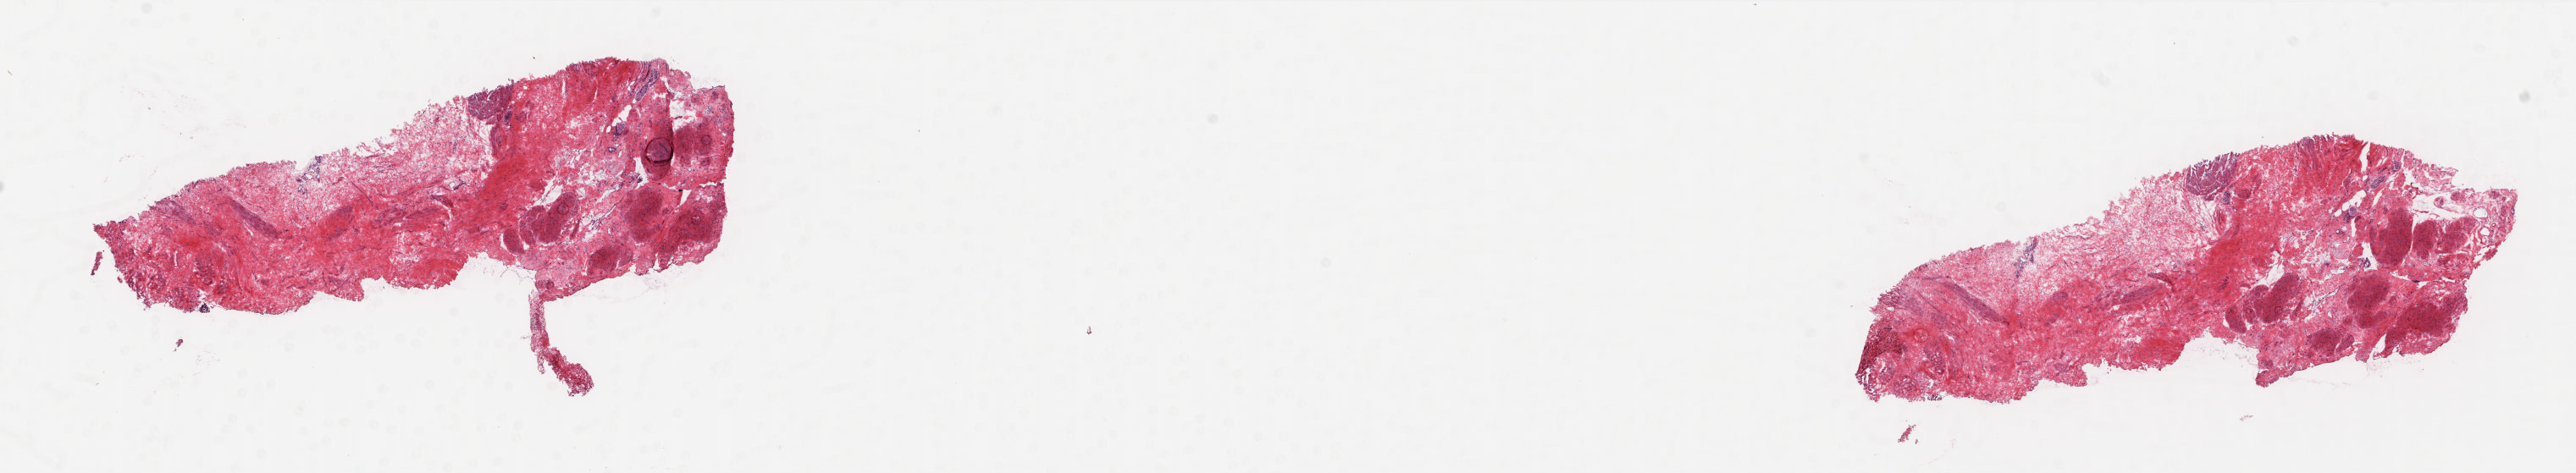
H&E-stained whole-slide image — a low-resolution overview of the entire scanned area, about 24.5 x 4.5 mm (acquisition: 20x scan); frozen section from the top of the tissue portion; bladder, solid tissue normal (non-tumour tissue) sample. Patient: female, age at initial diagnosis 75 years. Pathologist review of this section (percent, as recorded): tumour cells 0%, tumour nuclei 0%, normal cells 100%, stromal cells 0%, necrosis 0%. Infiltration values recorded for this section: lymphocyte infiltration 0%, monocyte infiltration 0%, neutrophil infiltration 0%.
This section: solid tissue normal sample (biorepository sample class). Patient diagnosis: Transitional cell carcinoma.